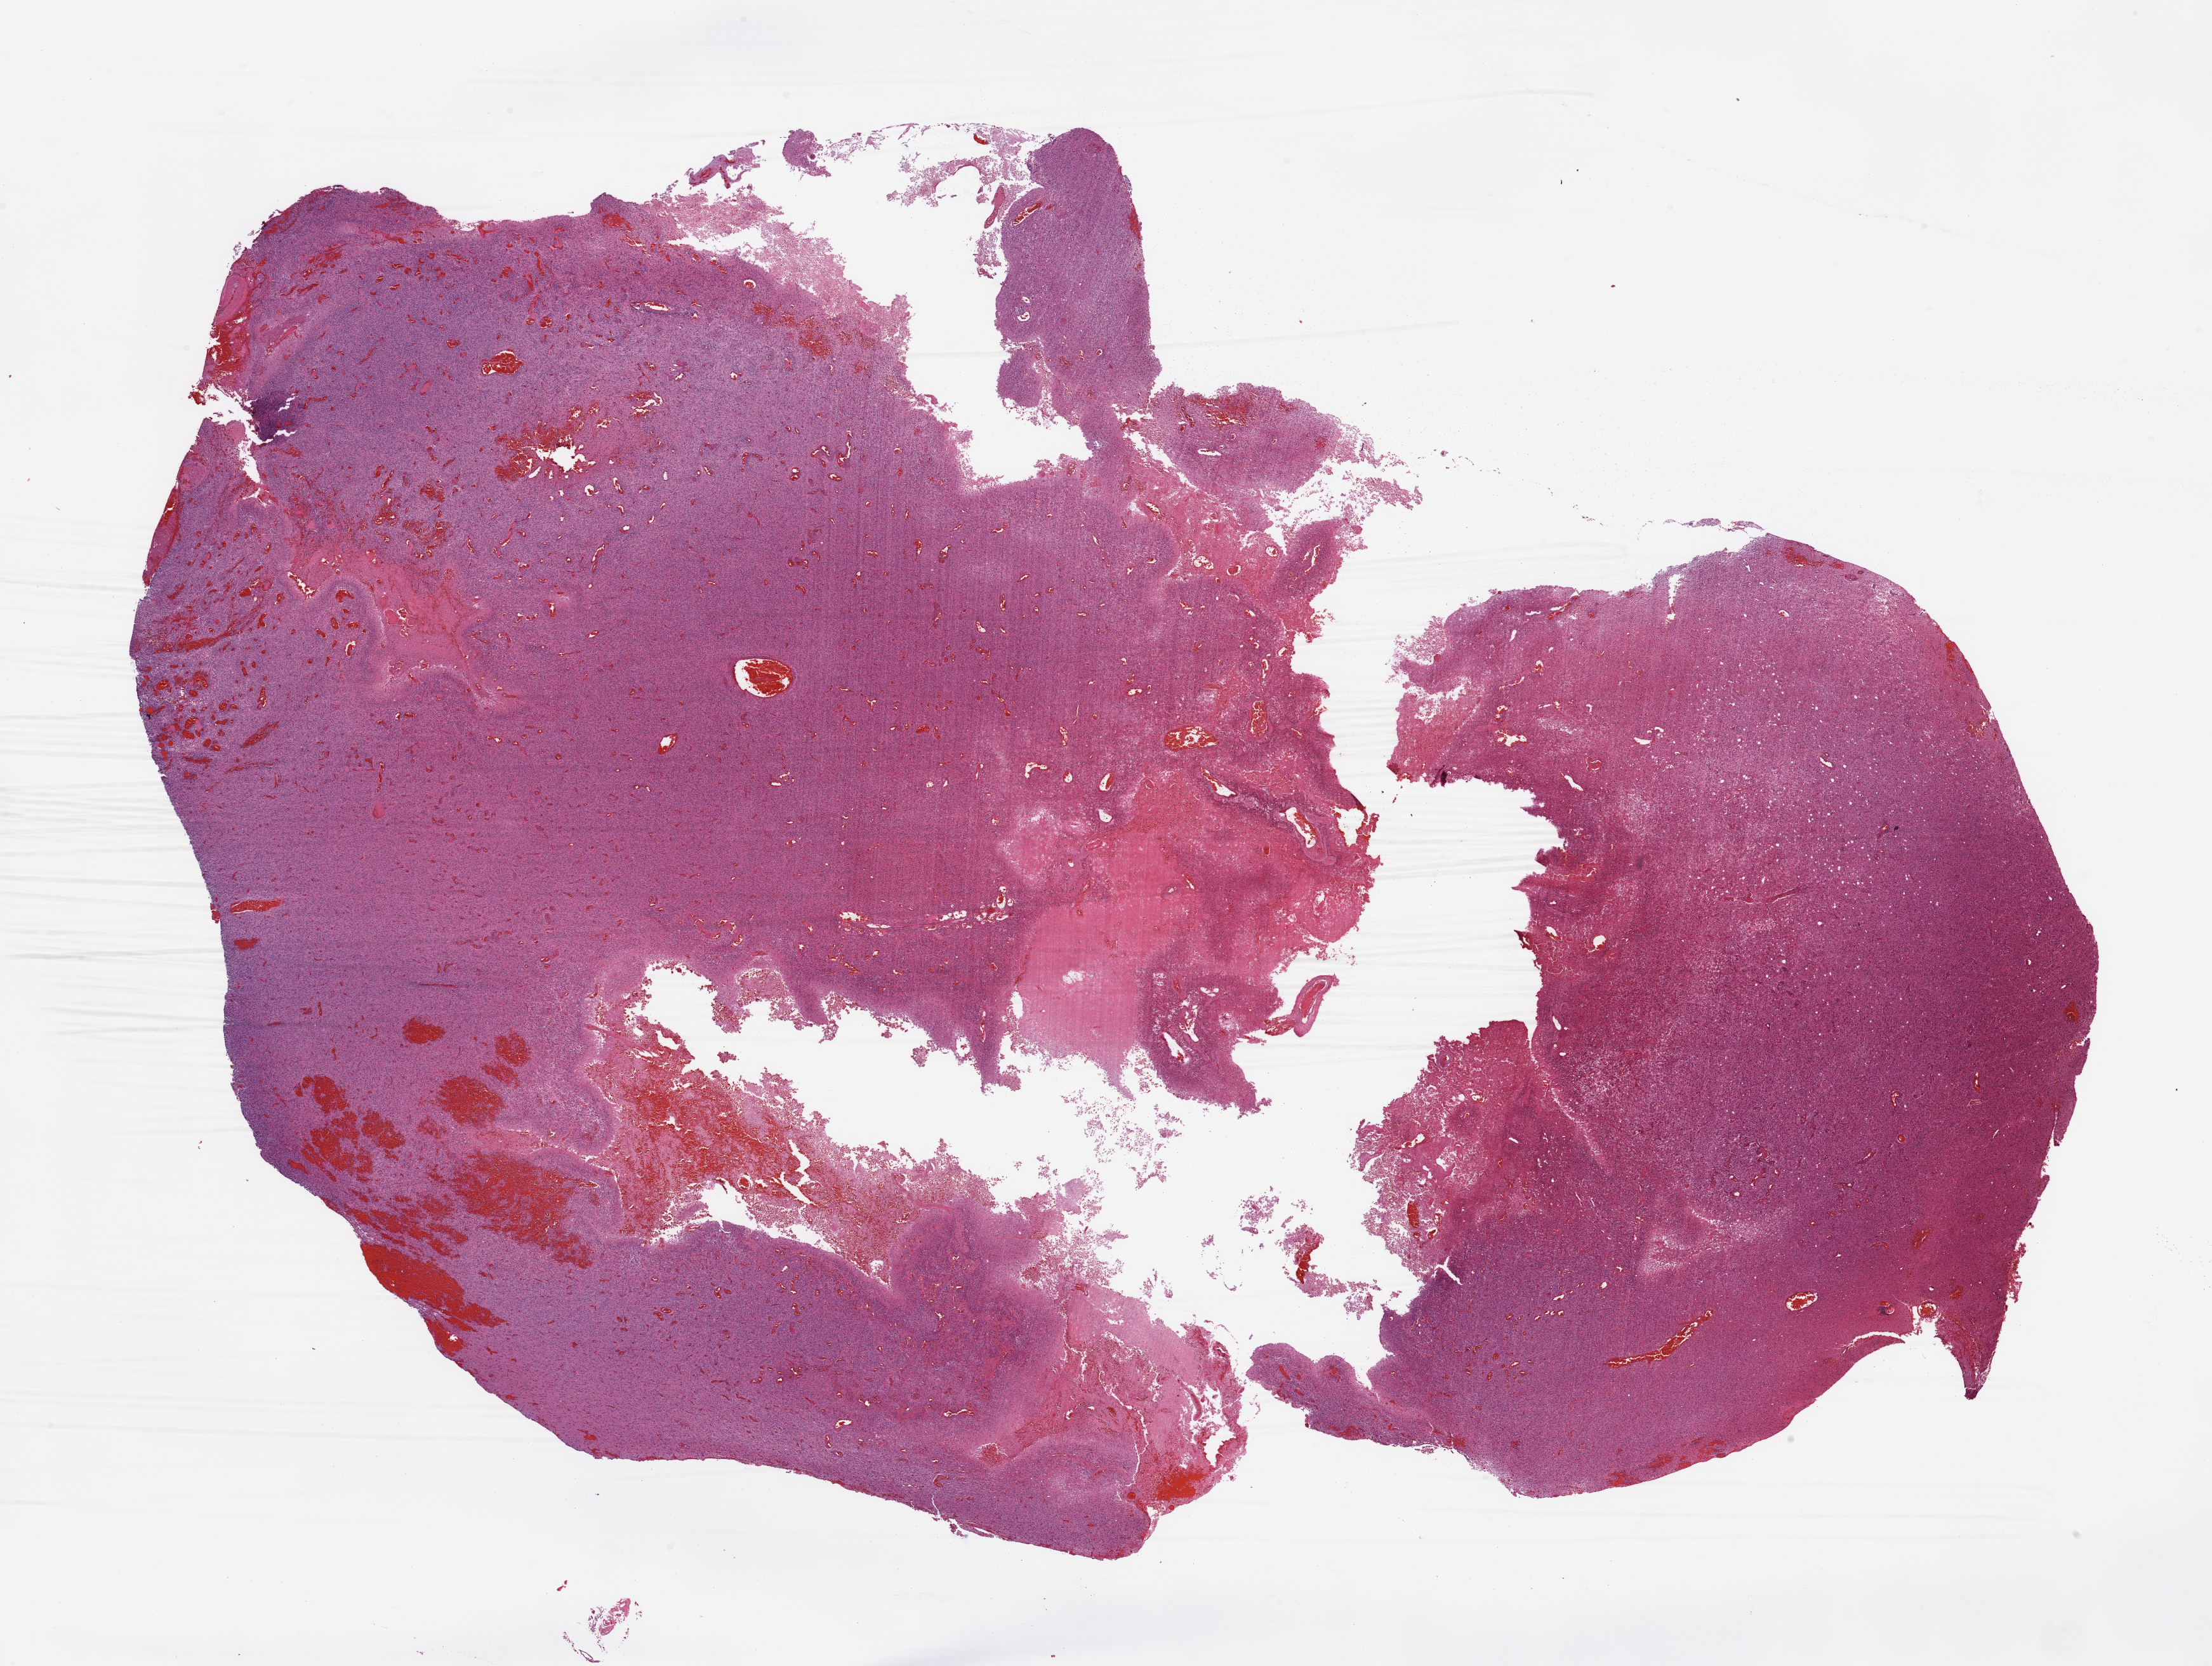
H&E-stained whole-slide image — low-resolution overview of the scanned area, about 27.6 x 20.8 mm, tumour tissue sample, brain. Patient: female, age 64 years.
Diagnosis: Glioblastoma. Primary tumour site (as recorded): frontal lobe.